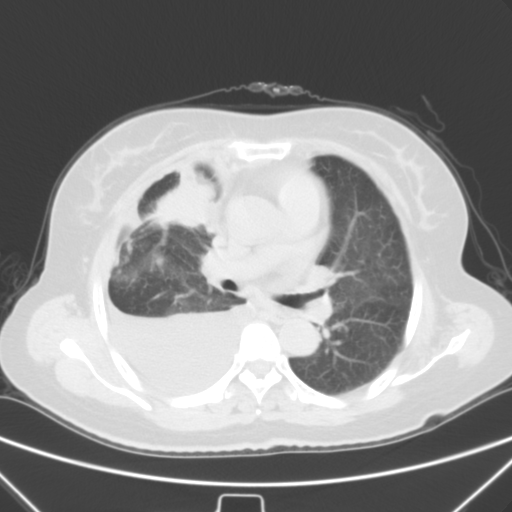
Chest CT, one axial slice; position 35 of 55 along the scan axis; lung window (W 1500 / L -600 HU); 512 × 512 image matrix, field of view 352 × 352 mm. Female patient, age 66 years. From the clinical record (not read from this slice): clinical TNM (as recorded): T2 N0 M1.
Annotated regions visible in this slice (rectangle marked by the reading radiologist):
- lung tumour (recorded histology: adenocarcinoma): bounding box <151,174,213,230> (left, top, right, bottom; pixels)